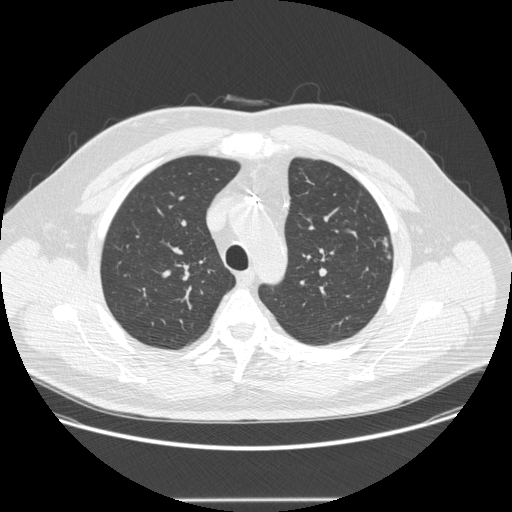
Chest CT (low-dose screening protocol), one axial image. First (baseline) screen. Lung window (W 1500 / L -600 HU). 1.25 mm slice thickness. Standard (soft-tissue) reconstruction kernel (STANDARD). 120 kVp. 512 × 512 image matrix. Male participant, aged 55 years at enrolment. Former smoker at enrolment.
• Expert-annotated lung lesion, bounding box <373,233,402,263> (left, top, right, bottom; pixels).
• Screening reader's record for this exam (one nodule recorded; not confirmed to be the boxed lesion): non-calcified nodule or mass ≥4 mm, left upper lobe, 5 × 4 mm, smooth margins, soft tissue attenuation.
• Official screen result: positive, change unspecified: nodule(s) >= 4 mm or enlarging nodule(s), mass(es), or other non-specific abnormalities suspicious for lung cancer.